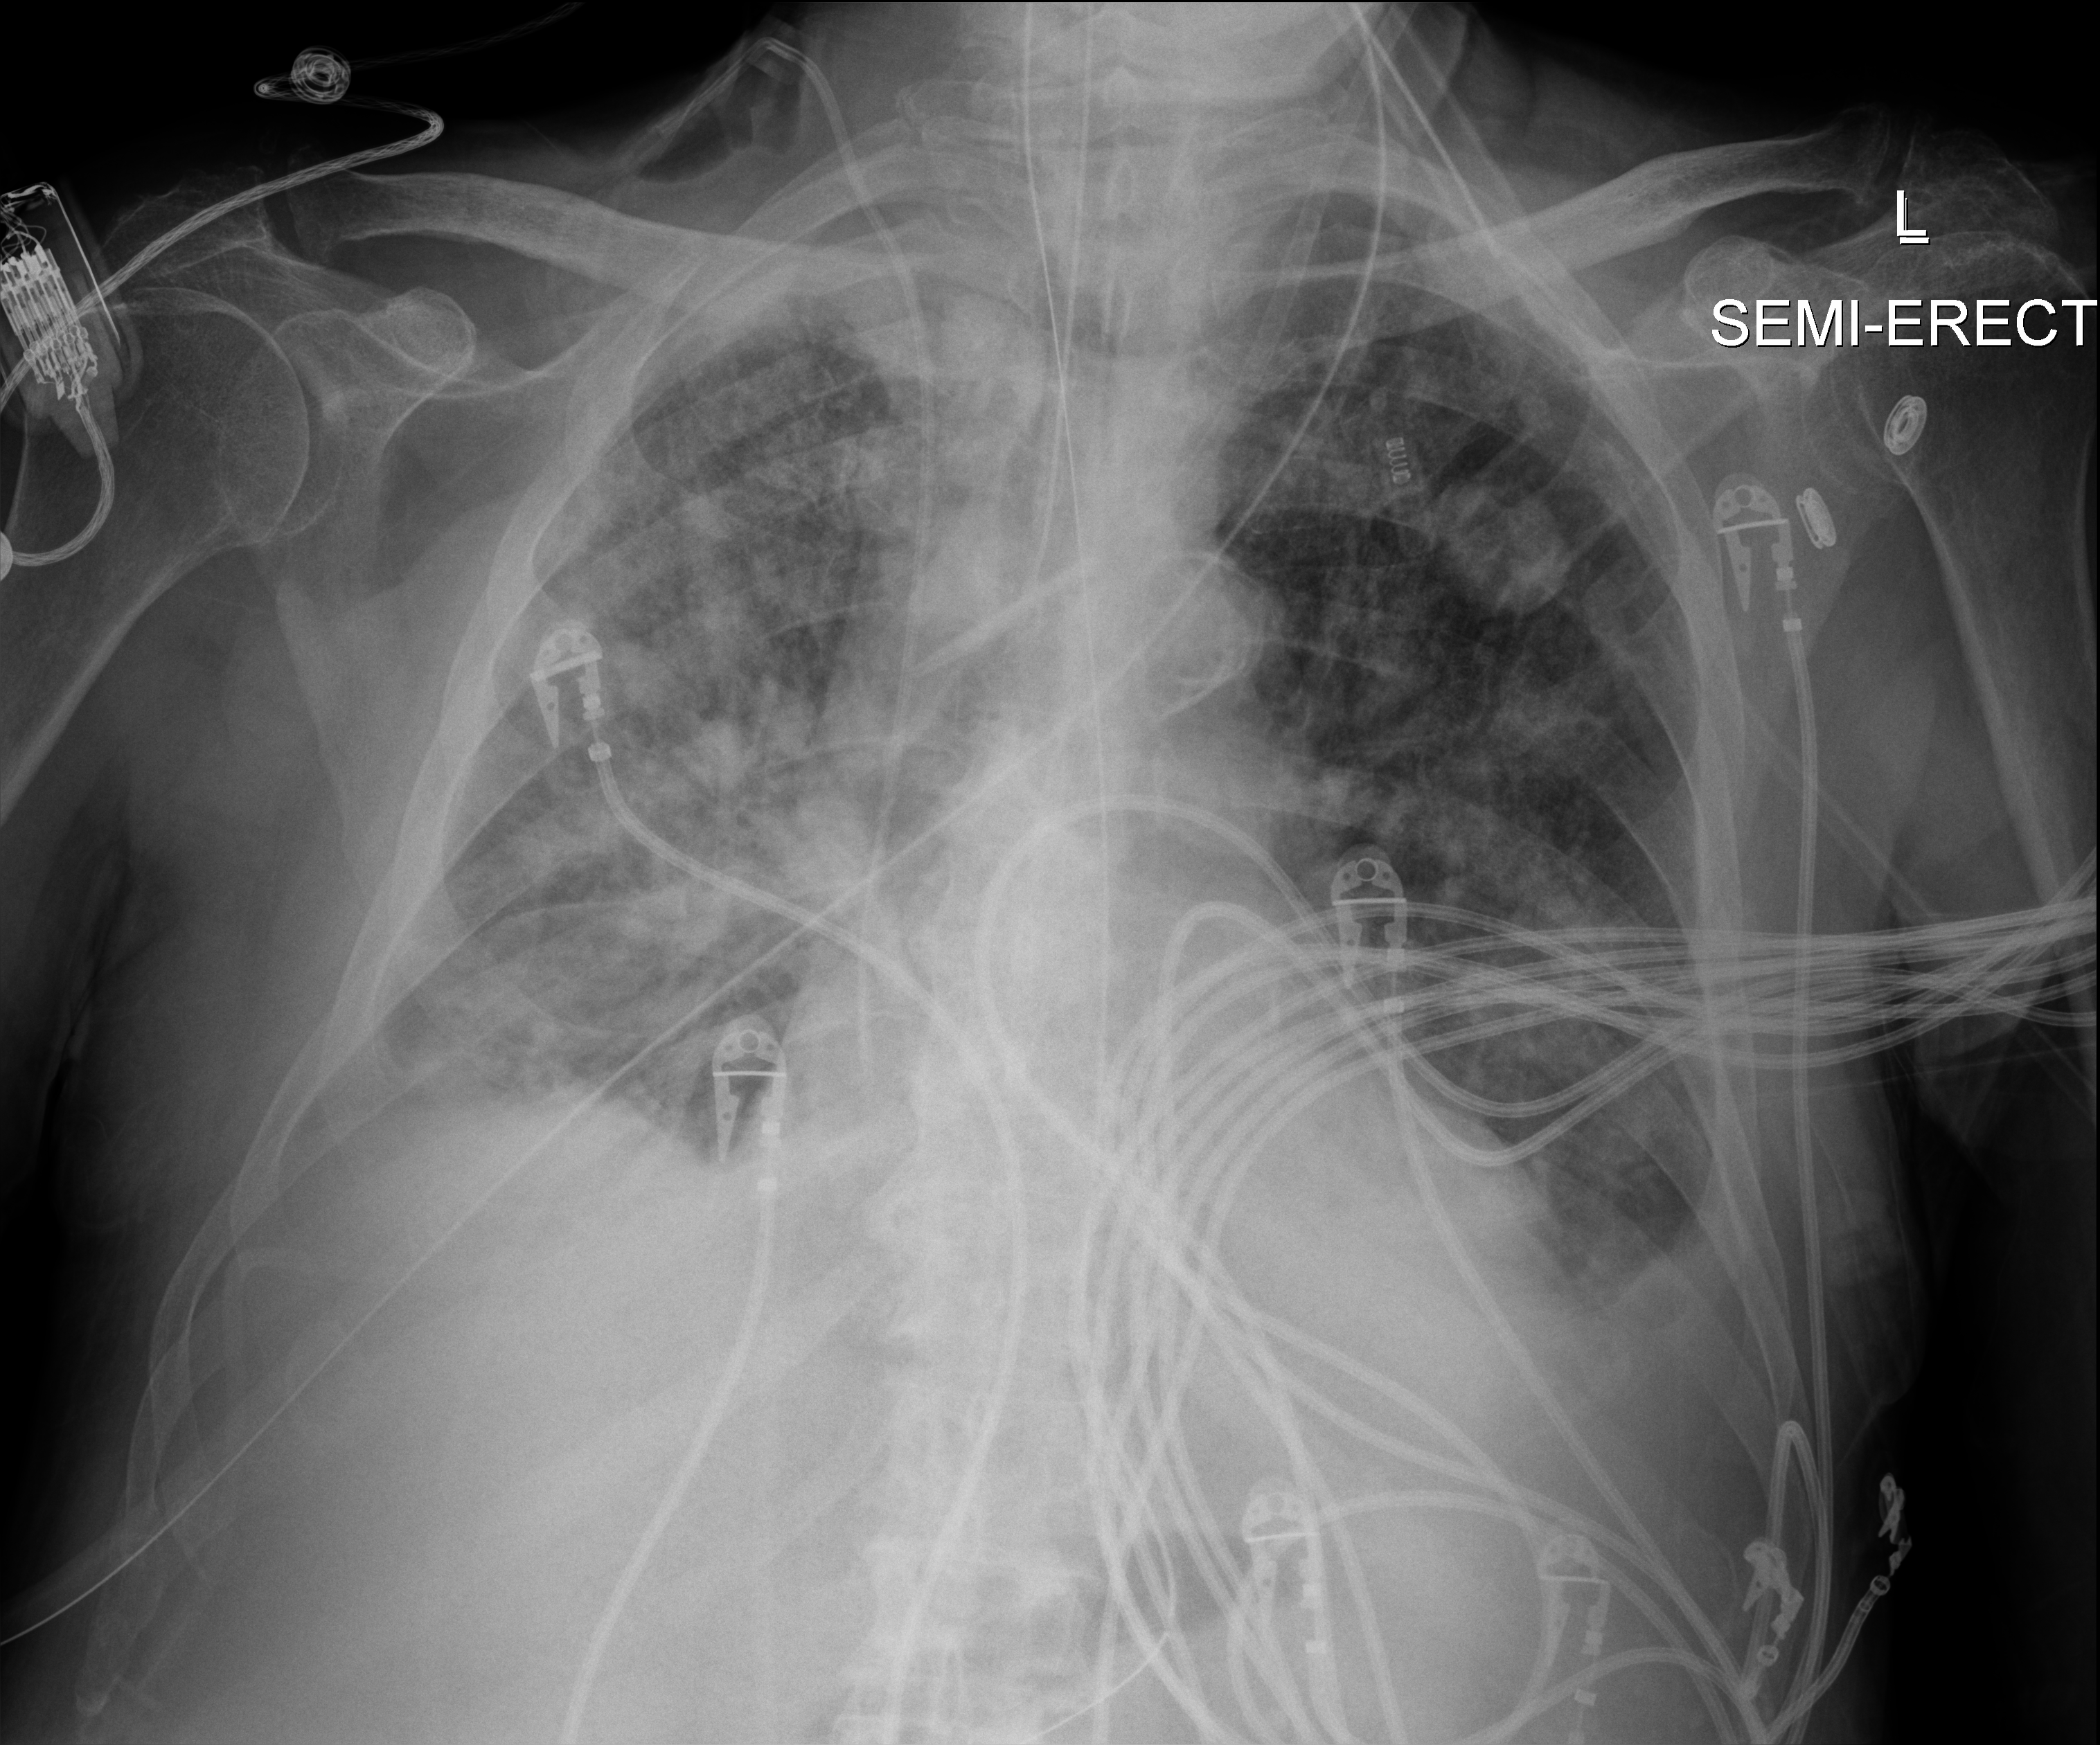
Portable chest radiograph. Patient hospitalised with COVID-19; male, aged 75–90 years.
Hospital-stay facts (about this admission, not read from this image; timing relative to this image not recorded): admitted to intensive care during this hospital stay: yes.